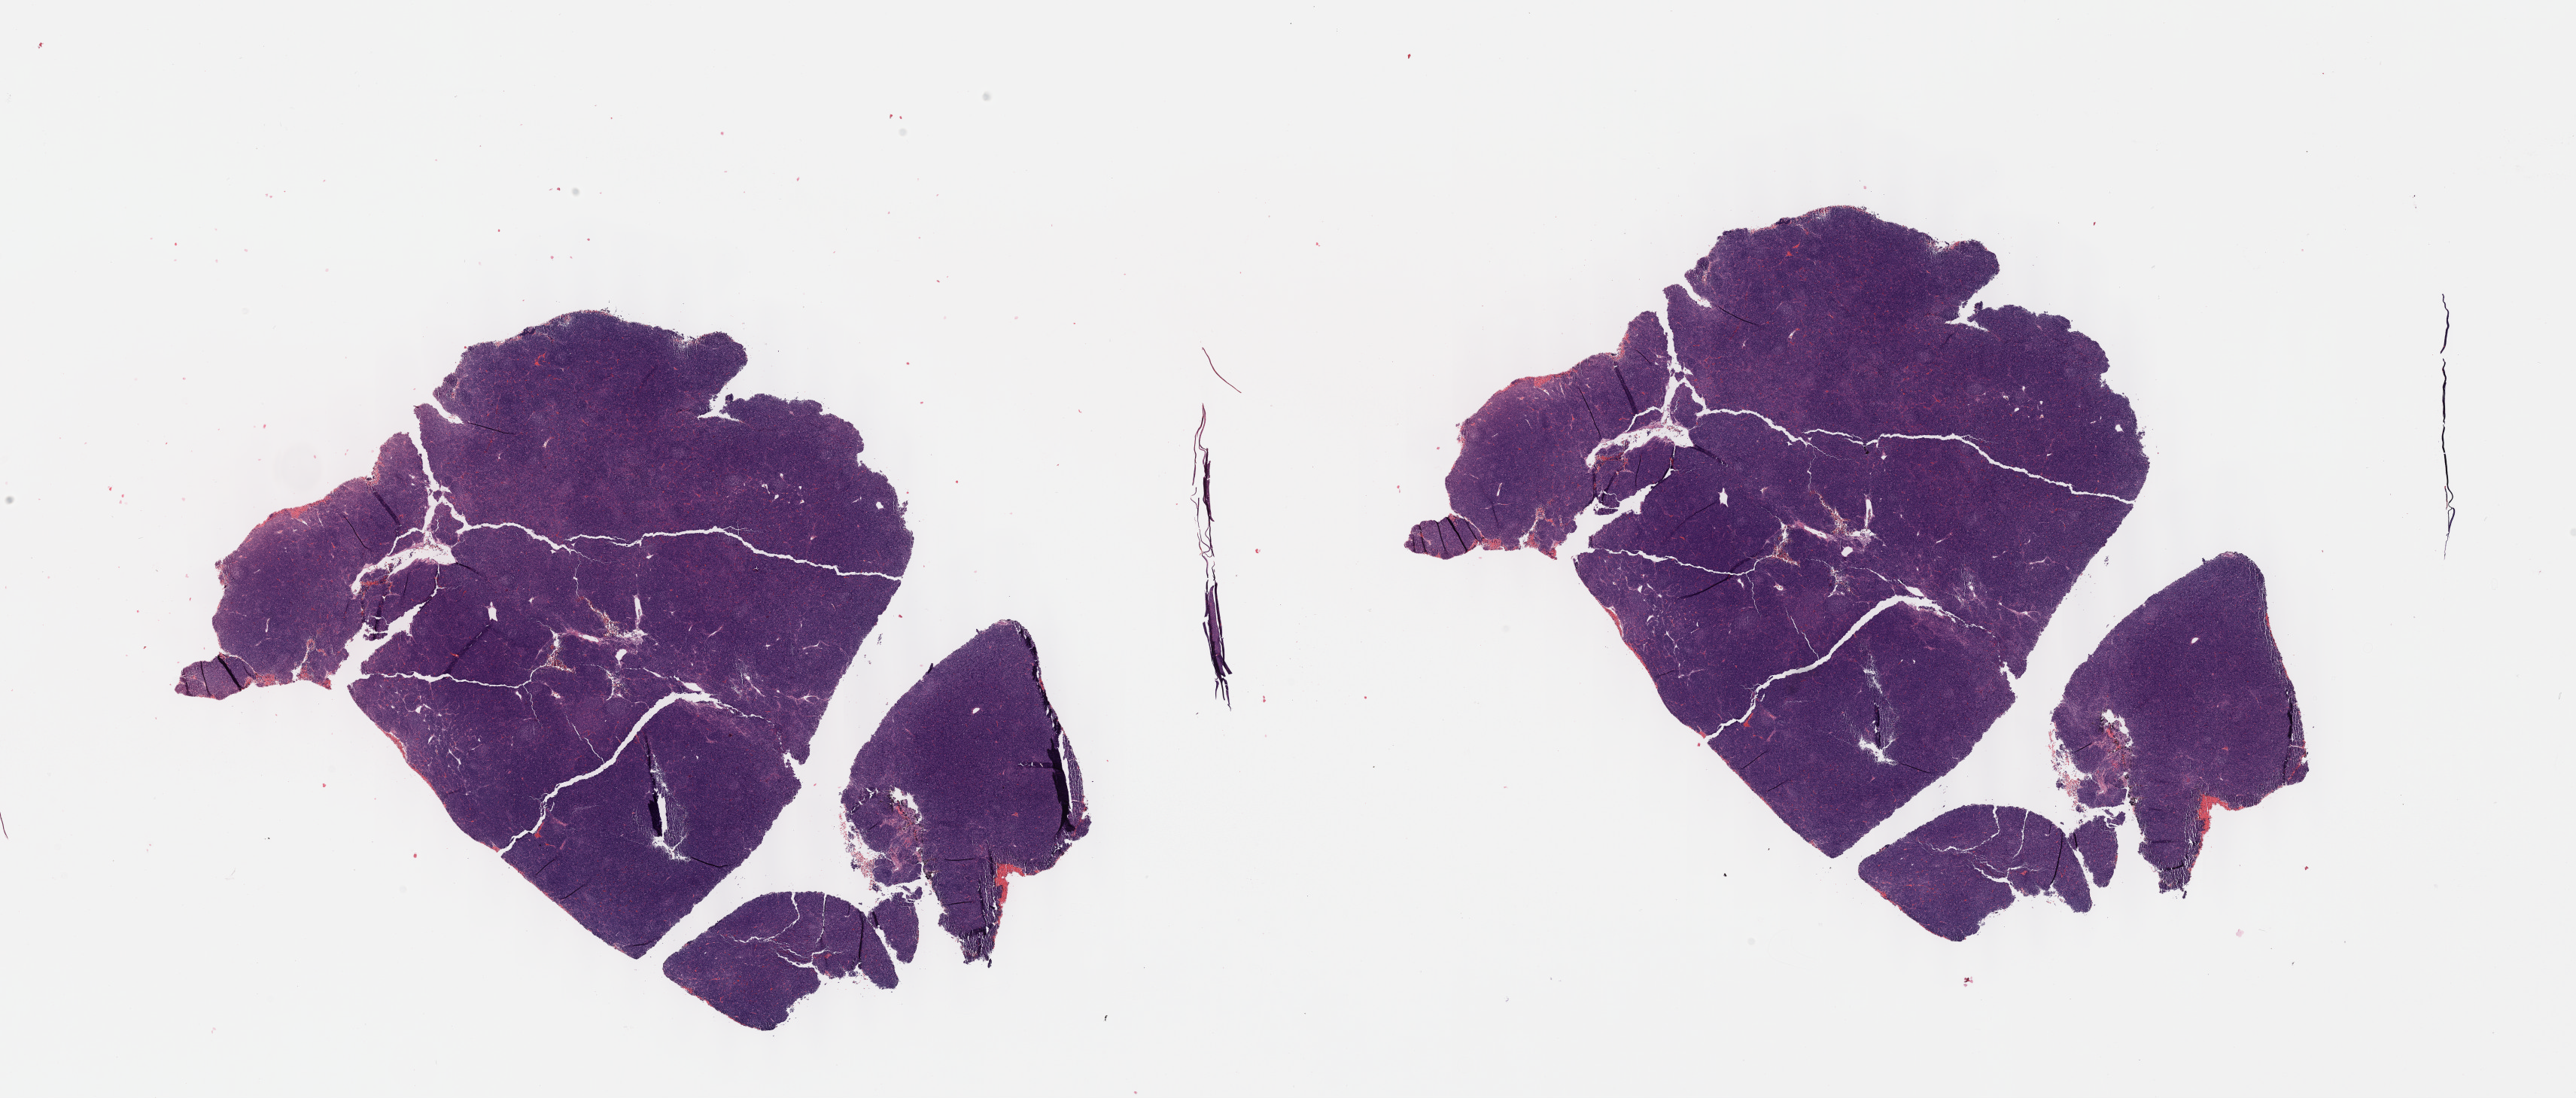
Whole-slide histology image, Hematoxylin and eosin (H&E) stained — low-resolution overview of the scanned area, about 27.7 x 11.8 mm; formalin-fixed paraffin-embedded (FFPE) diagnostic section; thymus, primary tumour sample. Male, age 40 years at initial diagnosis.
• pathologic diagnosis: Thymoma, type AB, malignant